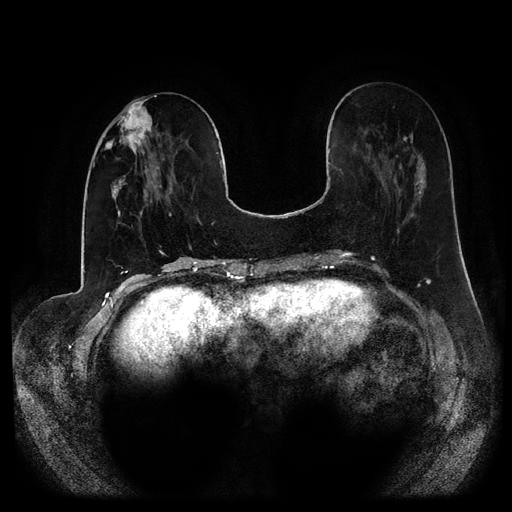
Breast MRI (dynamic contrast-enhanced, multi-phase), one axial slice. Slice 34 of 116 in the series (ordered by position). Dynamic contrast-enhanced series, time point 2 of 5 at this slice position (early post-contrast). 1.5 T. TE 2.6 ms, TR 5.2 ms. 2 mm slice thickness. 512 × 512 image matrix, field of view 380 × 380 mm. Female patient, age 53 years.
Outlined on this slice (semi-automatically segmented with operator editing):
- breast lesion (labelled 'tumour' in the annotation; benign lesions carry a separate 'benign' label): box from (x=104, y=97) to (x=154, y=155) px